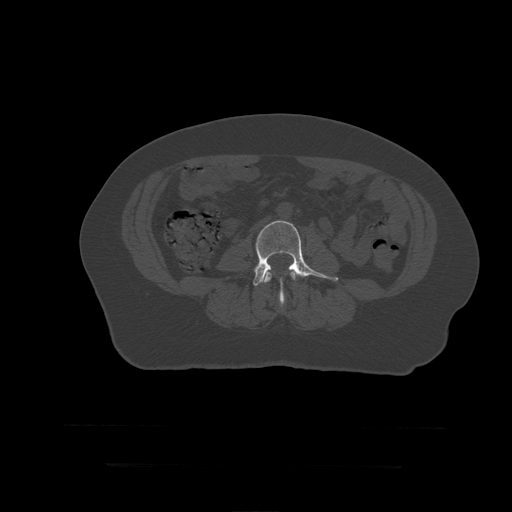
CT including the spine, one axial slice; slice 104 of 399 in the series (ordered by position); bone window (W 1800 / L 400 HU); 1.25 mm slice thickness; 512 × 512 image matrix, field of view 450 × 450 mm. Patient age 41 years. From the clinical record (not read from this slice): primary cancer: breast.
Annotated regions visible in this slice (semi-automatic segmentation, software-assisted and operator-edited):
- L3 vertebra: bounding box [x1, y1, x2, y2] px = [264, 272, 296, 283]
- L4 vertebra: [230, 221, 339, 307]